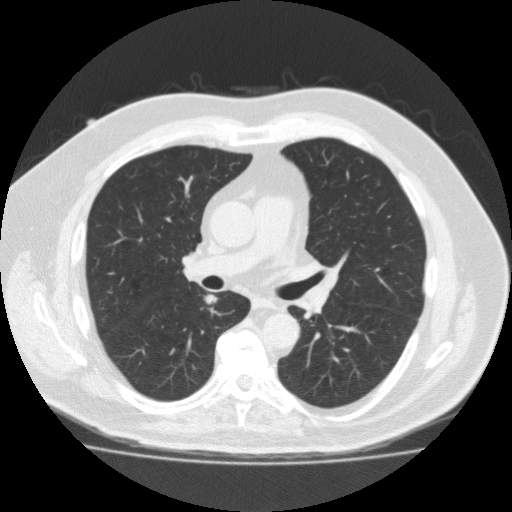
Low-dose screening chest CT, one axial slice. Position 111 of 183 along the scan axis. Reconstruction kernel FC10. 120 kVp. Lung window (W 1500 / L -600 HU). 2 mm slice thickness. 512 × 512 image matrix, field of view 391 × 391 mm.
Annotated regions visible in this slice (outlined manually by an expert reader):
- lesion 1 (tumor, lower lobe of right lung): bounding box (x1, y1, x2, y2) in pixels: (206, 295, 217, 304)